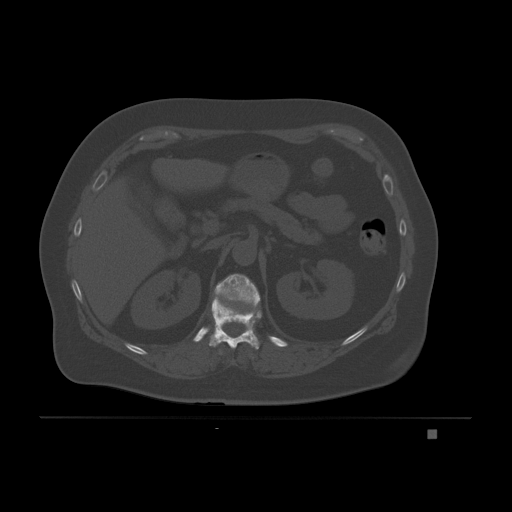
CT including the spine, one axial slice. Position 88 of 221 along the scan axis. Bone window (W 1800 / L 400 HU). 3 mm slice thickness. 512 × 512 image matrix. Female patient, age 63 years. Case-level facts recorded for this patient, not image findings: primary cancer: breast.
Annotated regions visible in this slice (semi-automatically segmented with operator editing):
- T11 vertebra: bounding box [x1, y1, x2, y2] px = [209, 298, 262, 350]
- T12 vertebra: [214, 274, 260, 308]